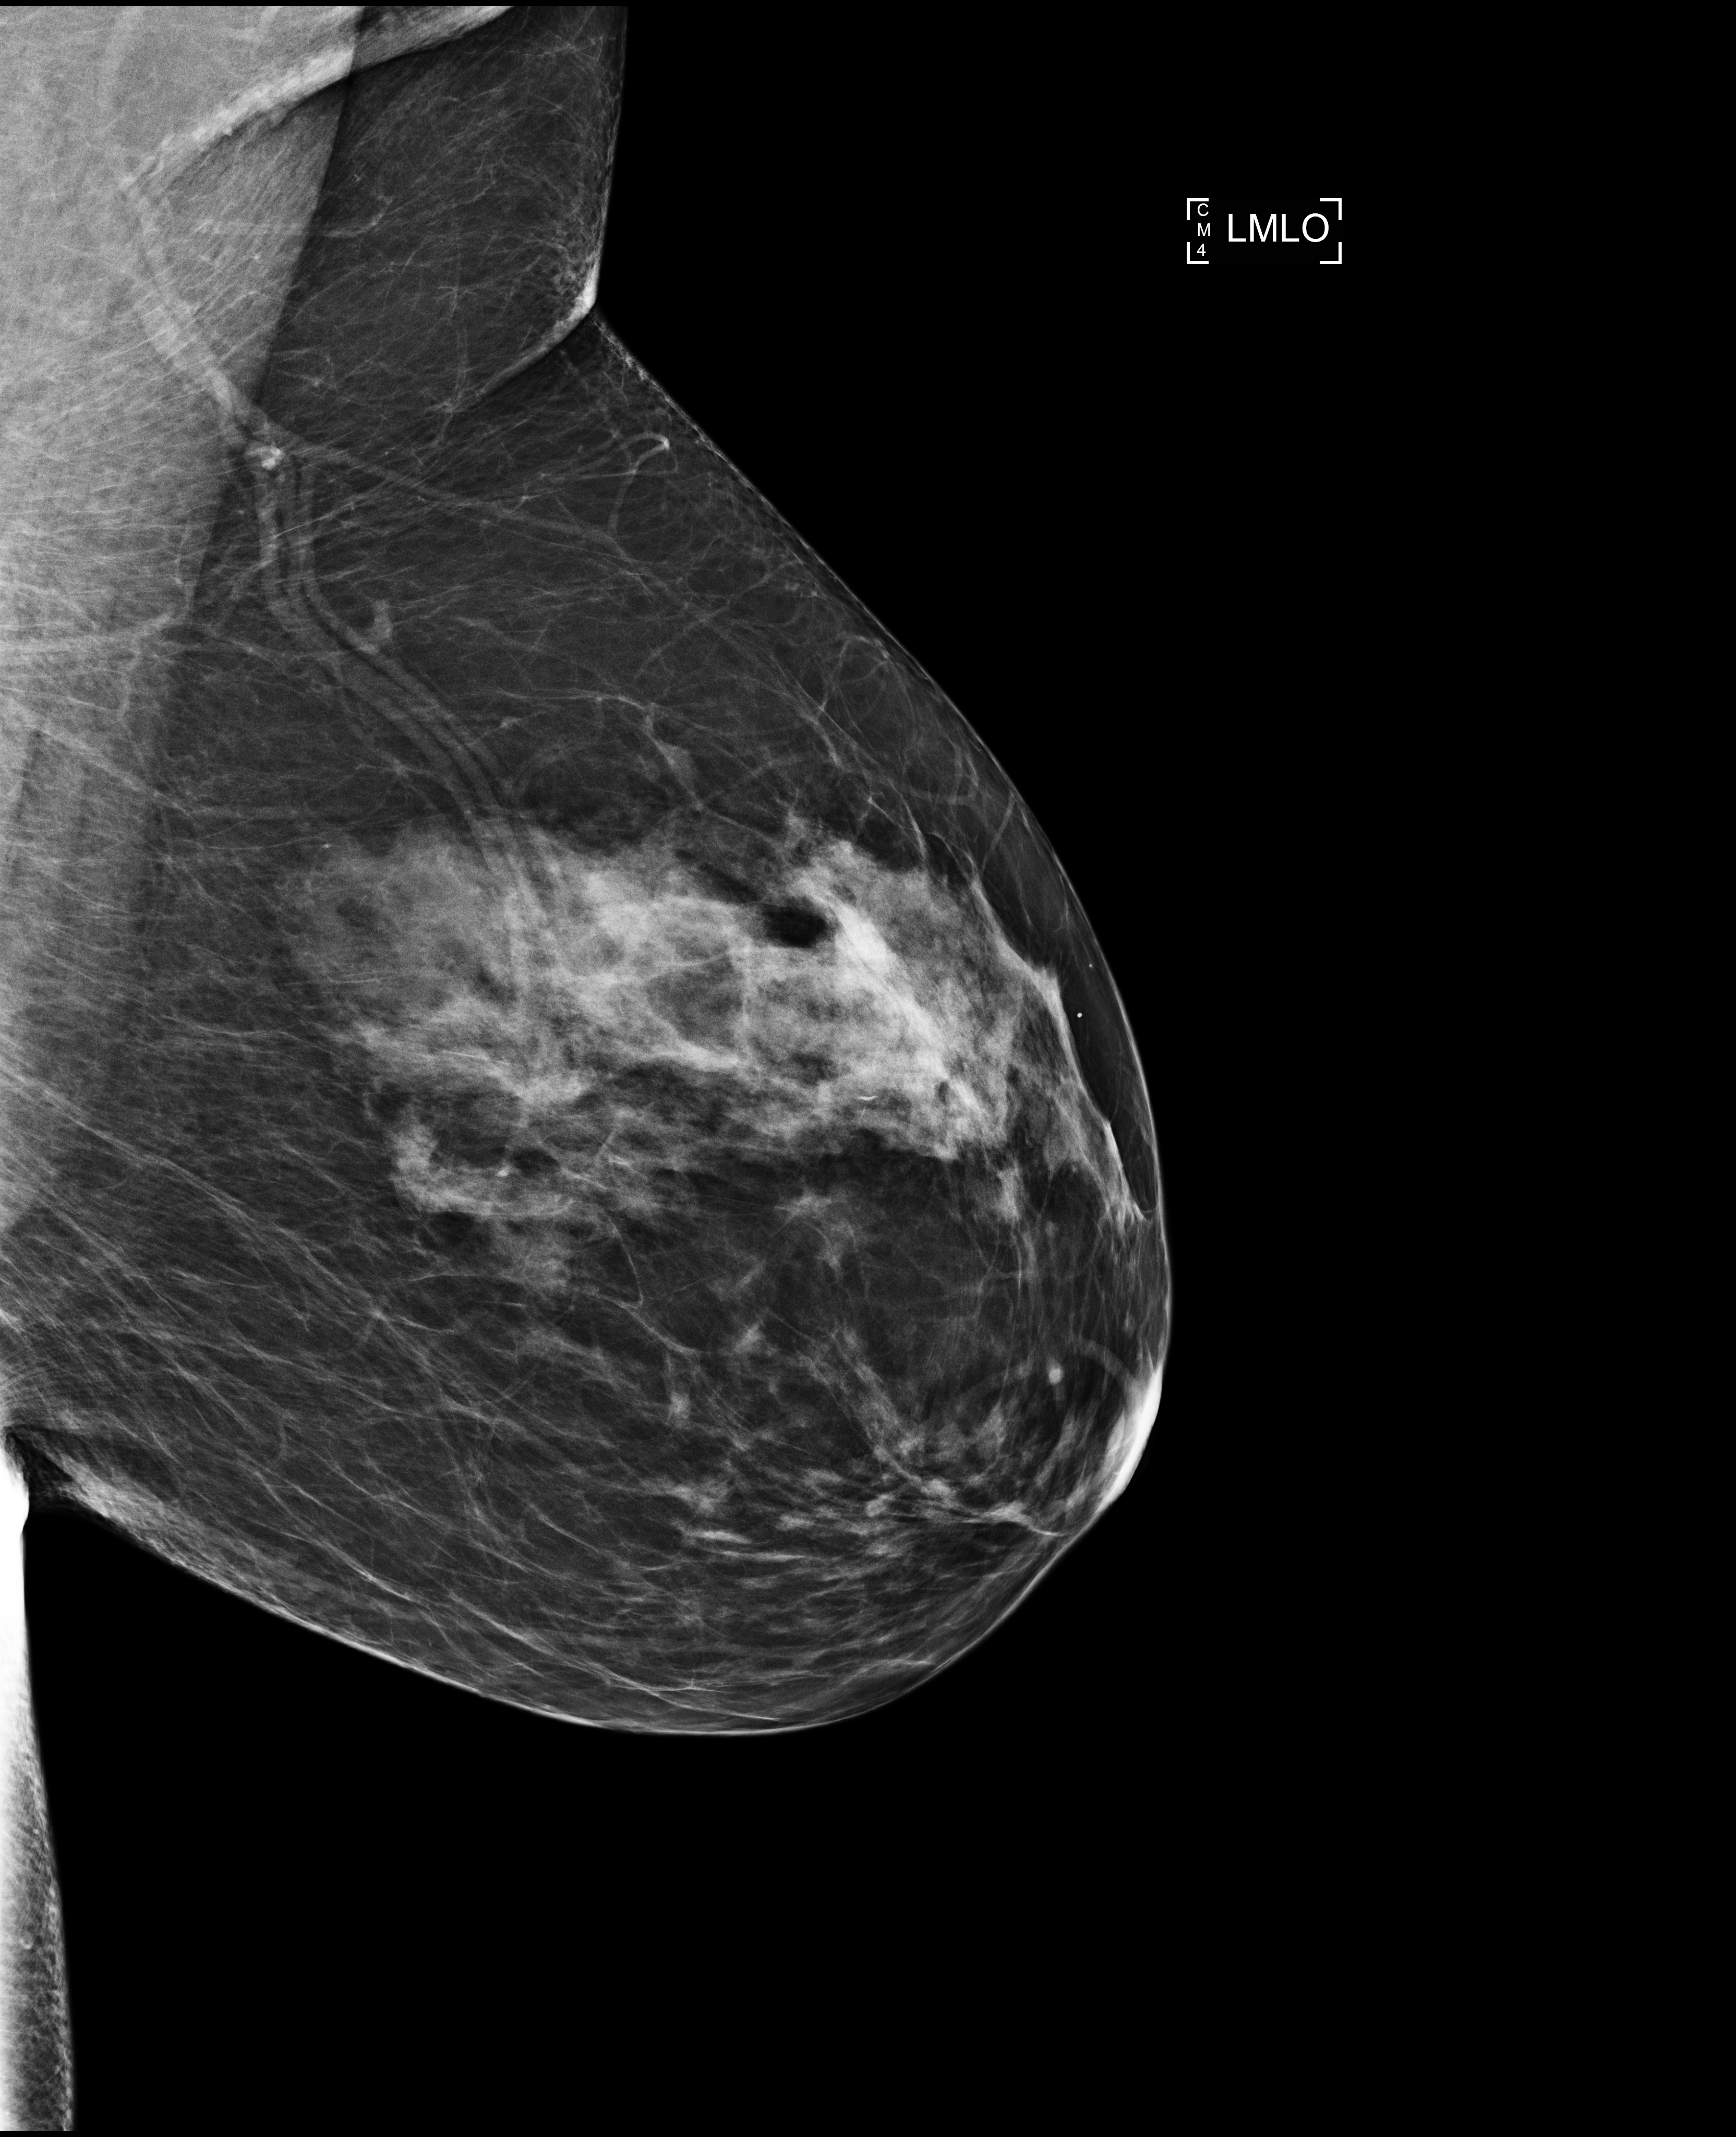
Digital mammogram (FFDM); left breast; MLO view; annual screening mammography examination. Female patient, age 55 years.
Breast density at the screening exam (both breasts): heterogeneously dense (BI-RADS density category c). Final BI-RADS assessment for this screening round (tomosynthesis exam, both breasts): category 1. Recall: no recall after this screen.